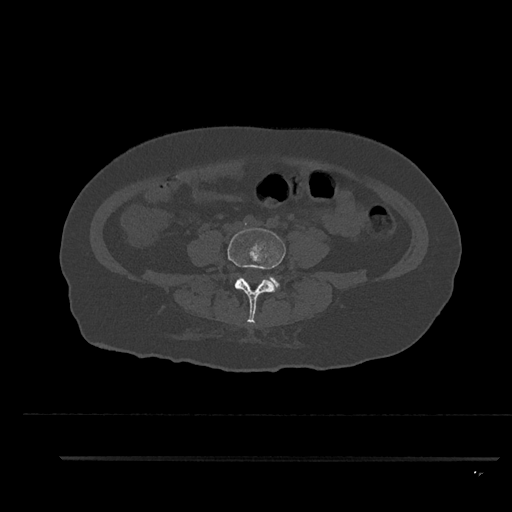
CT including the spine, one axial slice; slice 6 of 797 in the series (ordered by position); reconstruction kernel Br40s/3; 120 kVp; bone window (W 1800 / L 400 HU); 0.5 mm slice thickness; 512 × 512 image matrix, field of view 408 × 408 mm. Female patient, age 44 years. Case-level facts recorded for this patient, not image findings: primary cancer: renal; vertebrae with lytic lesions (as recorded): L1.
Outlined on this slice (semi-automatically segmented with operator editing):
- L4 vertebra: bounding box (x1, y1, x2, y2) in pixels: (227, 228, 286, 324)